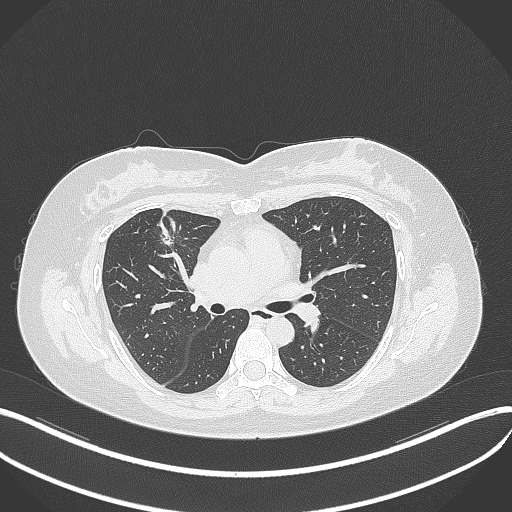
Chest CT, one axial slice; reconstruction kernel B70f; 120 kVp; lung window (W 1500 / L -600 HU); 1 mm slice thickness; 512 × 512 image matrix. Patient: female, 42 years. Case-level facts recorded for this patient, not image findings: clinical TNM (as recorded): T1b N0 M0.
Annotated regions visible in this slice (bounding box drawn by a radiologist):
- lung tumour (recorded histology: adenocarcinoma): bounding box (x1, y1, x2, y2) in pixels: (154, 225, 180, 245)